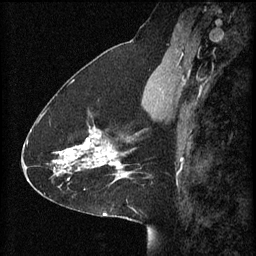
Breast MRI (dynamic contrast-enhanced), one sagittal slice. Slice 27 of 60 in the series (ordered by position). 3 images stored at this slice position (order not interpretable as contrast timing). 1.5 T. TE 4.2 ms, TR 8.2 ms. 2 mm slice thickness. 256 × 256 image matrix. Female patient, age 41 years.
Annotated regions visible in this slice (semi-automatically segmented with operator editing):
- analysis volume of interest (the breast-tissue region the enhancement analysis was run in; not a lesion): bounding box <58,114,128,181> (left, top, right, bottom; pixels)
- tumour enhancement mask (voxels above the 70 % enhancement threshold inside the analysis volume of interest): <58,128,128,181>